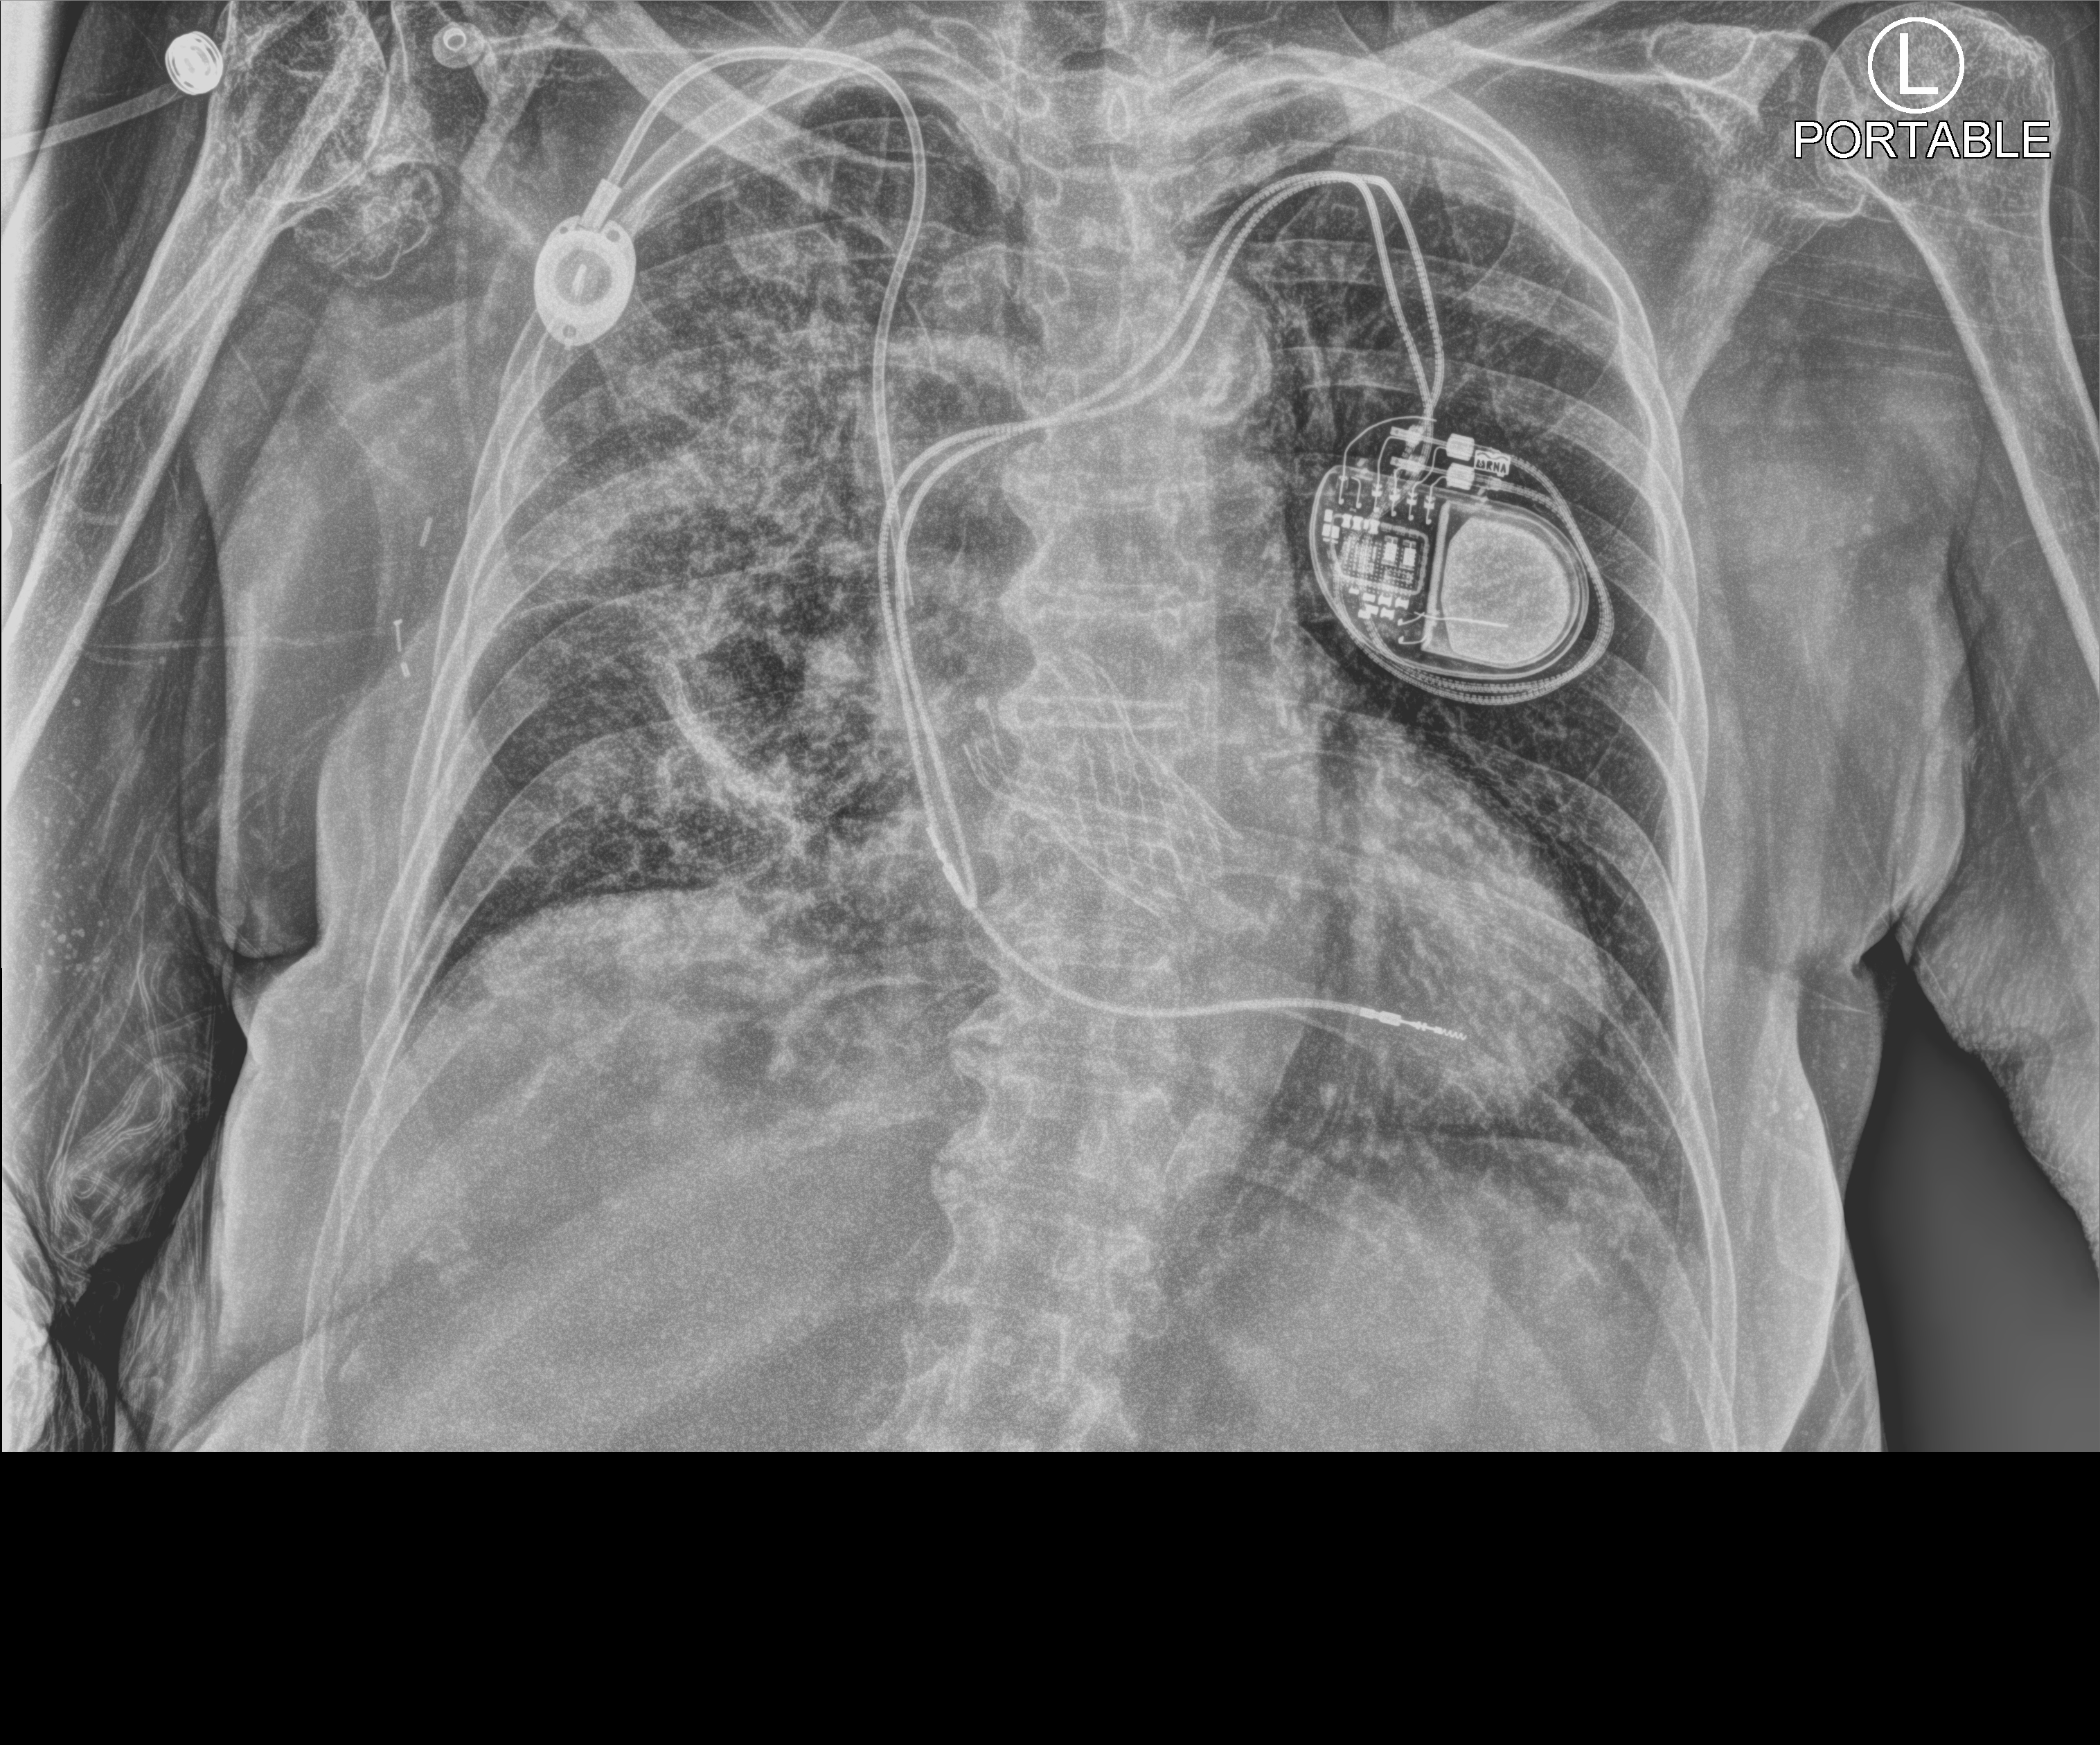
Portable chest radiograph; anteroposterior (AP) projection. Patient hospitalised with COVID-19; female, aged 75–90 years.
Admission-level facts for this patient (not findings on this image; timing relative to this image not recorded): mechanically ventilated during this hospital stay: no; admitted to intensive care during this hospital stay: no.